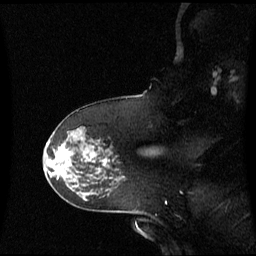
Breast MRI (dynamic contrast-enhanced), one sagittal slice; position 43 of 60 along the scan axis; dynamic contrast-enhanced series, image 2 of 3 at this slice position (ordered by acquisition); 1.5 T; TE 4.2 ms, TR 8.4 ms; 2.3 mm slice thickness; 256 × 256 image matrix, field of view 260 × 260 mm. Patient: female, 60 years. From the clinical record (not read from this slice): setting: breast cancer imaged before/during neoadjuvant chemotherapy; receptor status: HR-positive, HER2-negative.
Outlined on this slice (semi-automatically segmented with operator editing):
- analysis volume of interest (the breast-tissue region the enhancement analysis was run in; not a lesion): bounding box [x1, y1, x2, y2] px = [46, 141, 76, 171]
- tumour enhancement mask (voxels above the 70 % enhancement threshold inside the analysis volume of interest): [66, 153, 68, 156]